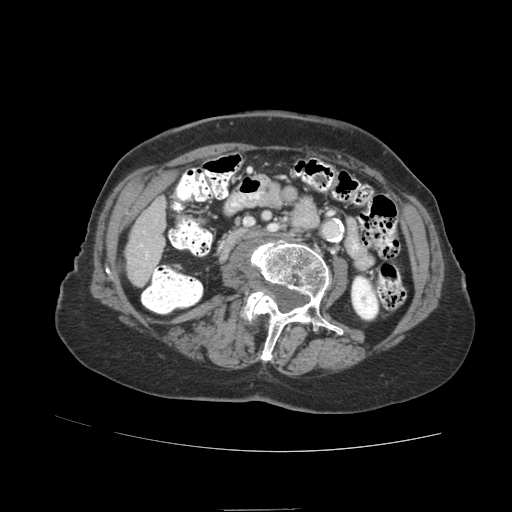
Contrast-enhanced abdominal CT (liver protocol), one axial slice. 140 kVp. Soft-tissue window (W 400 / L 40 HU). 2.5 mm slice thickness. 512 × 512 image matrix, field of view 360 × 360 mm. From the clinical record (not read from this slice): diagnosis: hepatocellular carcinoma (patient treated with transarterial chemoembolisation; whether this scan precedes or follows treatment is not stated here); TNM stage (as recorded): Stage-II; Child-Pugh class: A; tumour nodularity: multinodular; tumour size: 4 cm.
Structures marked on this image (semi-automatically segmented with operator editing):
- liver parenchyma outside the tumour (the mass and vessels are separate outlines, so this box may not span the whole liver): box from (x=126, y=174) to (x=171, y=286) px
- liver vessels: (x=139, y=244)–(x=149, y=259)